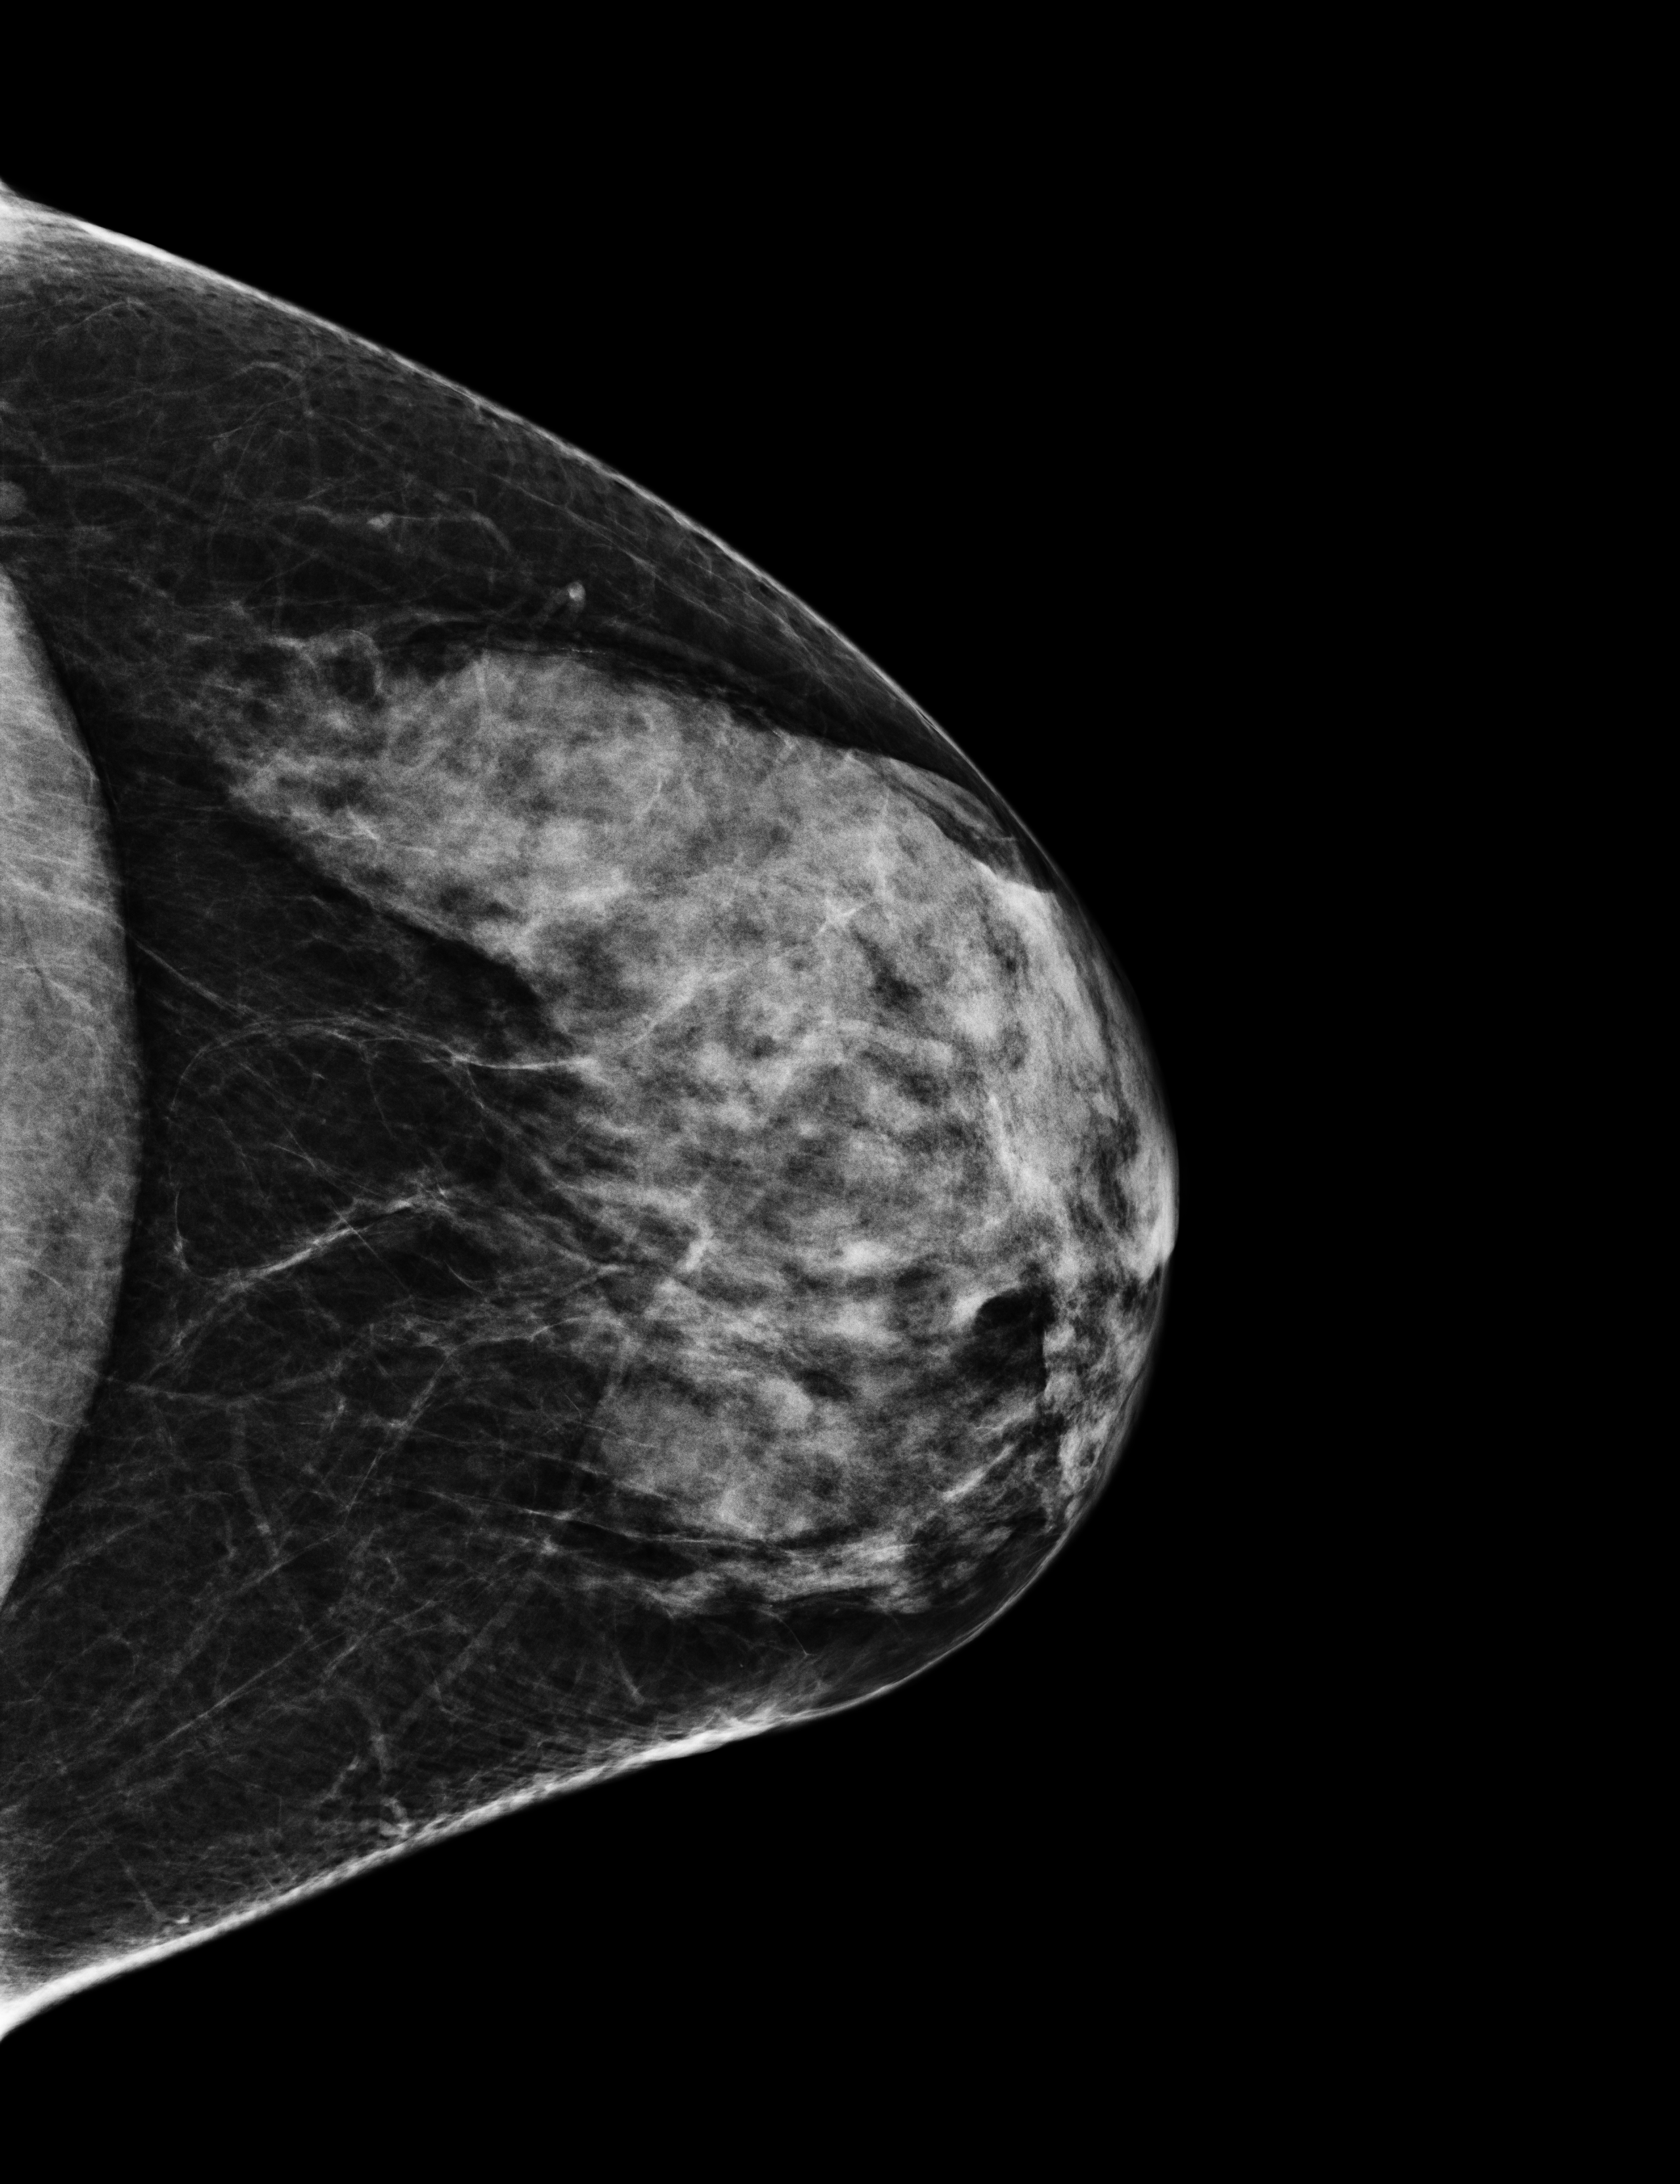
Digital mammogram (FFDM), left breast, CC view, screening examination, compressed breast thickness 55 mm. Female patient, age 54 years.
BI-RADS breast density category at the screening exam (both breasts, scale 1–4): 3. Final BI-RADS category for the screening round (tomosynthesis exam, both breasts): category 1. Recall: no recall after this screen.